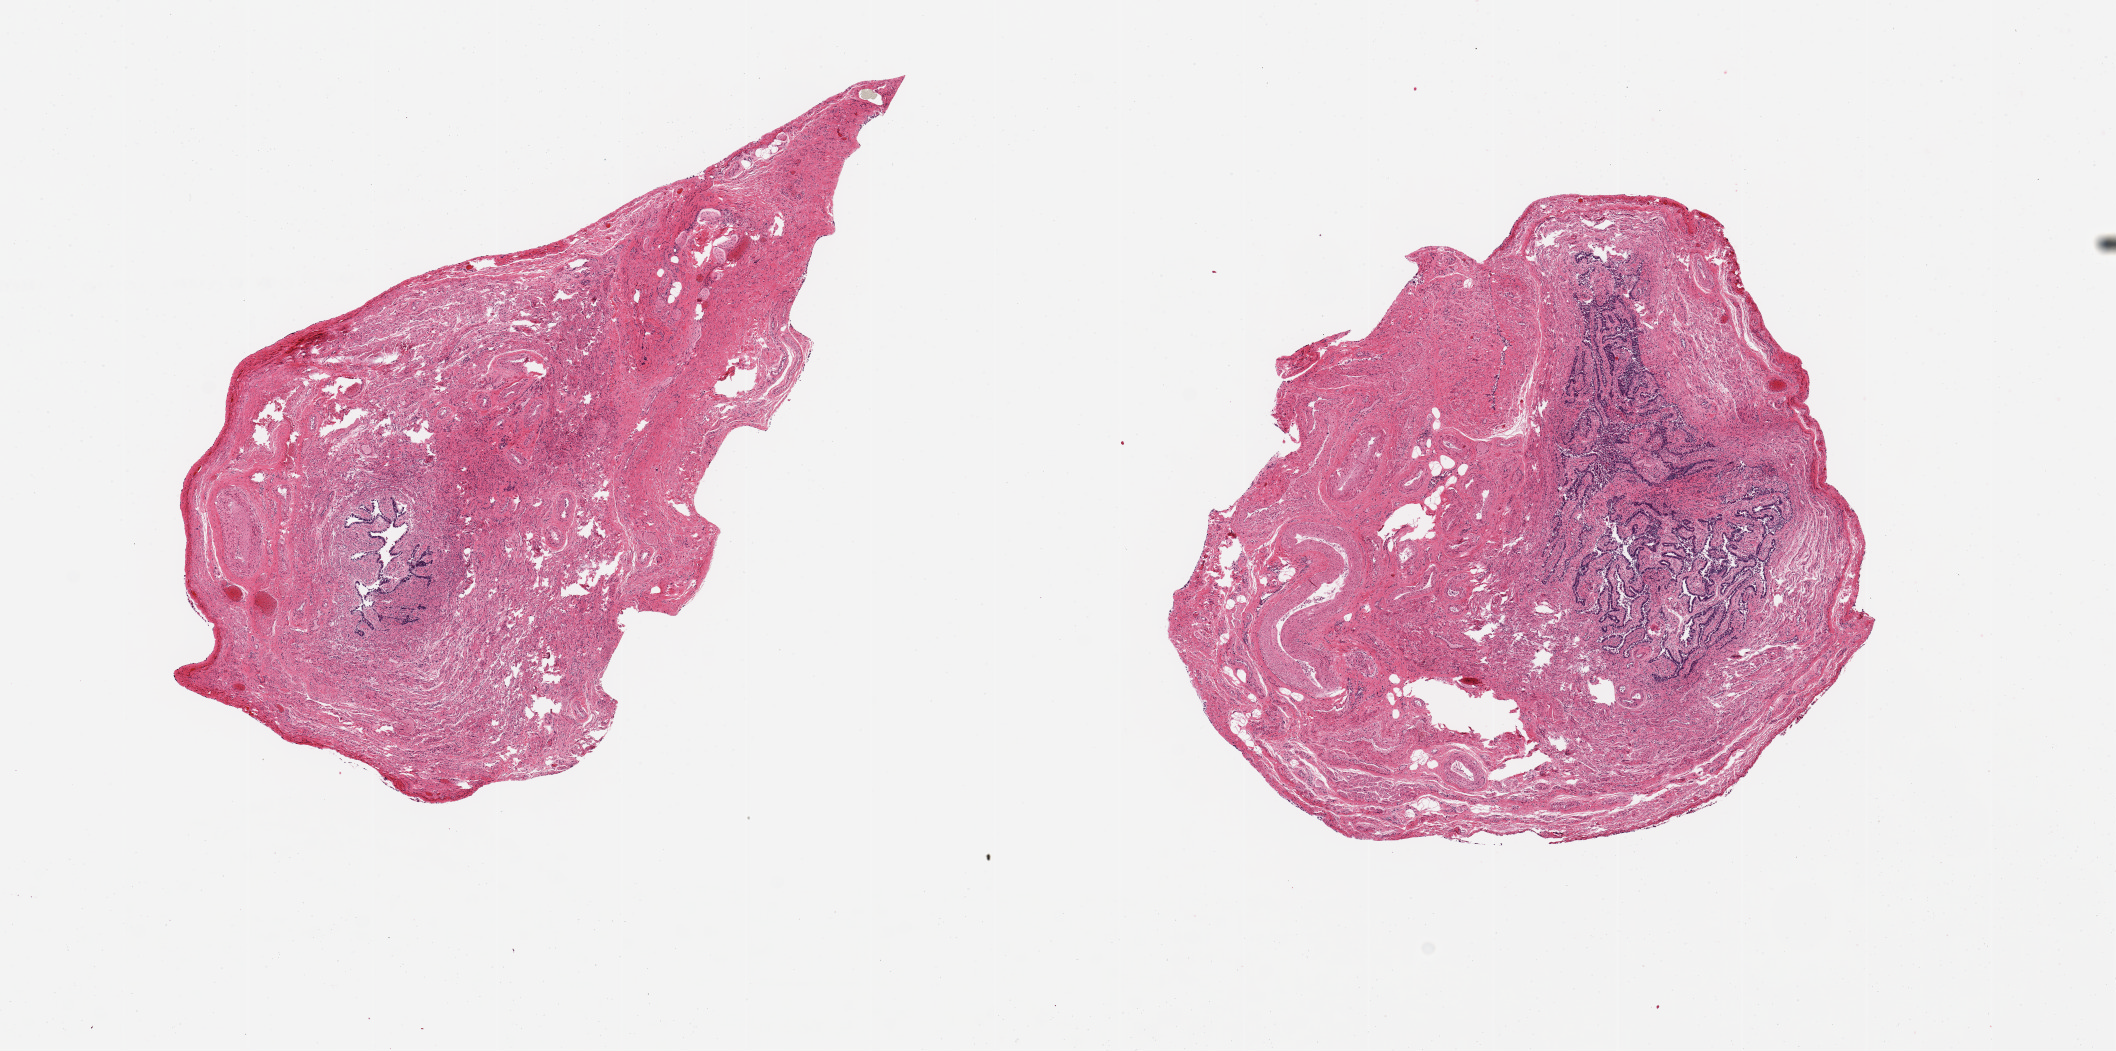
H&E whole-slide image — shown as a low-resolution overview of the whole scanned area (about 16.7 x 8.3 mm, acquisition: 20x scan); PAXgene-fixed paraffin-embedded (PFPE) section; sampled site (target tissue): fallopian tube; donor tissue sample.
• pathologist's review note for this sample: 2 ~6x4mm aliquots. Mucosa ~ 20% total; badly autolyzed